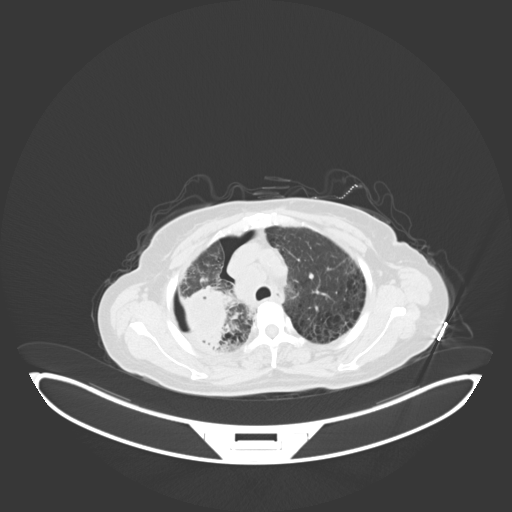
Chest CT, one axial slice. Position 47 of 69 along the scan axis. Reconstruction kernel B30f. Lung window (W 1500 / L -600 HU). 3 mm slice thickness. 512 × 512 image matrix. Female patient, age 64 years. Case-level facts recorded for this patient, not image findings: clinical TNM (as recorded): T3 N3 M0.
Annotated regions visible in this slice (rectangle marked by the reading radiologist):
- lung tumour (recorded histology: squamous cell carcinoma): bounding box [x1, y1, x2, y2] px = [173, 279, 239, 347]